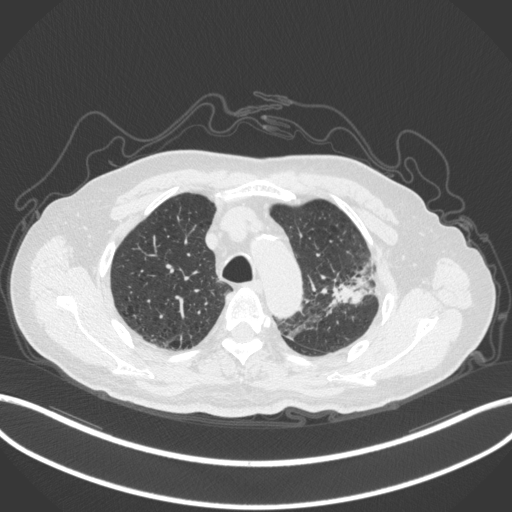
Chest CT, one axial slice. Position 231 of 331 along the scan axis. Lung window (W 1500 / L -600 HU). 1 mm slice thickness. 512 × 512 image matrix, field of view 400 × 400 mm. Patient: male, 79 years. From the clinical record (not read from this slice): clinical TNM (as recorded): T2a N1 M1.
Structures marked on this image (bounding box drawn by a radiologist):
- lung tumour (recorded histology: adenocarcinoma): bounding box (x1, y1, x2, y2) in pixels: (328, 253, 377, 313)